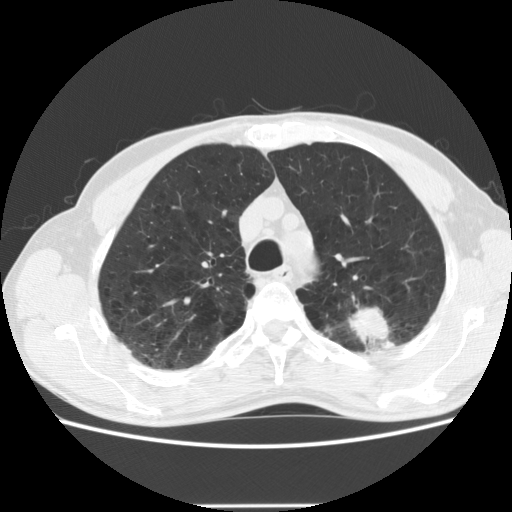
Low-dose screening chest CT, axial slice; baseline screening round; lung window (W 1500 / L -600 HU); 2.5 mm slice thickness; 512 × 512 image matrix. Male, age 64 years at enrolment. Current smoker at enrolment.
Lesion marked by an expert reader, bounding box <340,286,432,359> (left, top, right, bottom; pixels). The exam's reader record, not a measurement of the box and not confirmed to be the same lesion: non-calcified nodule or mass ≥4 mm, left upper lobe, 27 × 19 mm, poorly defined margins, soft tissue attenuation. Official screen result: positive, change unspecified: nodule(s) >= 4 mm or enlarging nodule(s), mass(es), or other non-specific abnormalities suspicious for lung cancer. Participant outcome: lung cancer diagnosed 23 days after this screen — adenocarcinoma, NOS, left upper lobe, moderately differentiated (G2), stage IA (AJCC 6th edition), 29 mm at pathology.